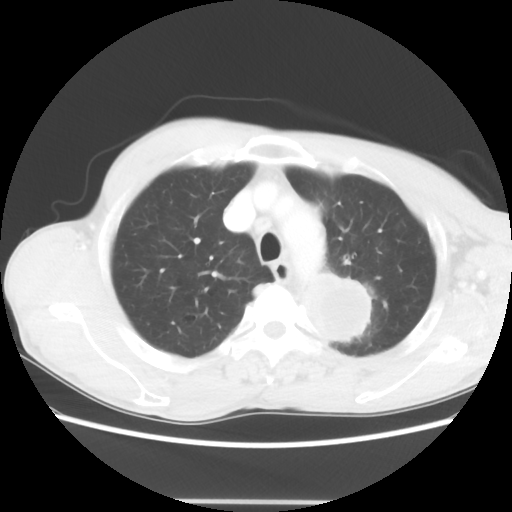
Chest CT, one axial slice. Position 51 of 62 along the scan axis. Reconstruction kernel STANDARD. Lung window (W 1500 / L -600 HU). 5 mm slice thickness. 512 × 512 image matrix, field of view 360 × 360 mm. Patient: male, 61 years. Case-level facts recorded for this patient, not image findings: clinical TNM (as recorded): T3 N1 M1.
Outlined on this slice (bounding box drawn by a radiologist):
- lung tumour (recorded histology: adenocarcinoma): bounding box <299,263,371,350> (left, top, right, bottom; pixels)